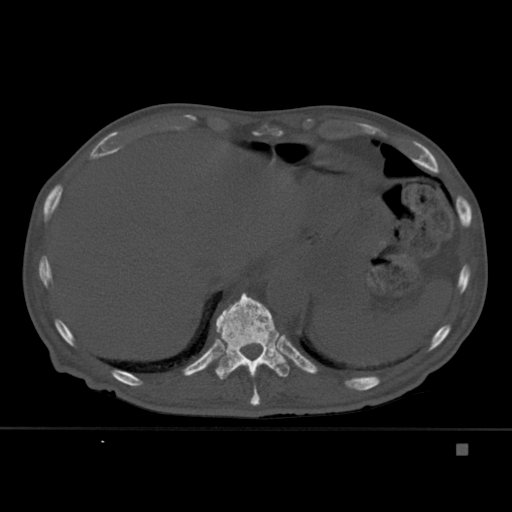
CT including the spine, one axial slice; position 220 of 451 along the scan axis; bone window (W 1800 / L 400 HU); 1.5 mm slice thickness; 512 × 512 image matrix, field of view 378 × 378 mm. Male patient, age 75 years. Case-level facts recorded for this patient, not image findings: primary cancer: prostate.
Structures marked on this image (semi-automatic segmentation, software-assisted and operator-edited):
- T10 vertebra: bounding box (x1, y1, x2, y2) in pixels: (248, 367, 260, 406)
- T11 vertebra: (215, 292, 290, 380)